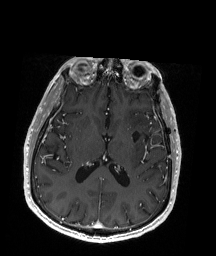
Brain MRI from a brain-tumour surgery series, one axial slice; position 89 of 192 along the scan axis; T1-weighted post-contrast; 1 mm slice thickness; 216 × 256 image matrix, field of view 211 × 250 mm. Case-level facts recorded for this patient, not image findings: histopathology: Oligodendroglioma; WHO grade: 2; IDH mutation: yes.
Outlined on this slice (manually delineated by an expert):
- previous resection cavity: box from (x=132, y=124) to (x=163, y=140) px